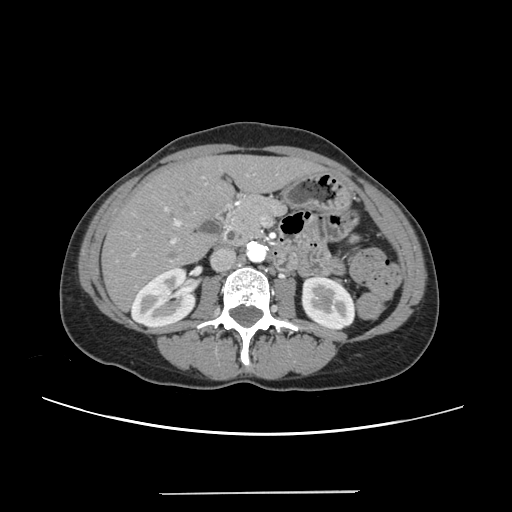
Contrast-enhanced abdominal CT, one axial slice. Position 105 of 240 along the scan axis. 120 kVp. Intravenous contrast given. Soft-tissue window (W 400 / L 40 HU). 1.25 mm slice thickness. 512 × 512 image matrix. Female patient, age 60 years. From the clinical record (not read from this slice): diagnosis: colorectal cancer liver metastases, imaged before liver resection; multiple liver metastases: no; largest metastasis: 1.5 cm; chemotherapy before resection: yes.
Structures marked on this image (manually delineated by an expert):
- liver: bounding box <104,157,317,308> (left, top, right, bottom; pixels)
- planned liver remnant (the part of the liver to remain after resection): <104,158,318,308>
- portal vein (with intrahepatic branches): <132,174,249,256>